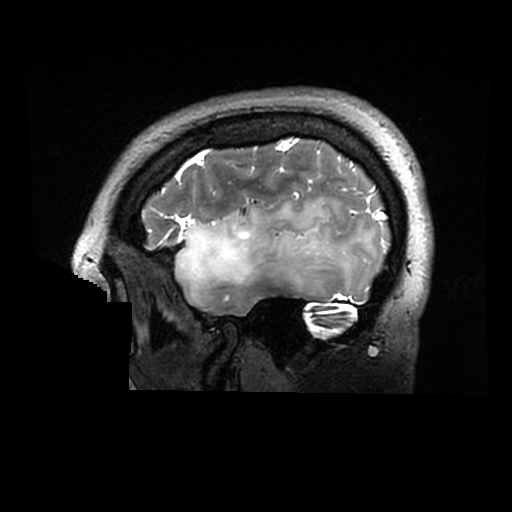
Brain MRI from a brain-tumour surgery series, one sagittal slice. Slice 237 of 320 in the series (ordered by position). 512 × 512 image matrix, field of view 240 × 240 mm. From the clinical record (not read from this slice): histopathology: Astrocytoma; WHO grade: 2; IDH mutation: yes.
Annotated regions visible in this slice (expert manual segmentation):
- tumour: bounding box (x1, y1, x2, y2) in pixels: (175, 198, 373, 299)